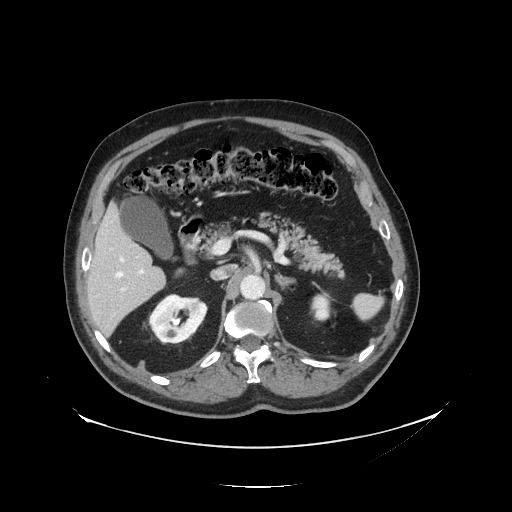
Contrast-enhanced abdominal CT, one axial slice; position 73 of 138 along the scan axis; intravenous contrast given; soft-tissue window (W 400 / L 40 HU); 2.5 mm slice thickness; 512 × 512 image matrix. Male patient, age 77 years. Case-level facts recorded for this patient, not image findings: diagnosis: colorectal cancer liver metastases, imaged before liver resection; multiple liver metastases: no; largest metastasis: 1.5 cm.
Outlined on this slice (expert manual segmentation):
- hepatic veins: box from (x=116, y=258) to (x=124, y=278) px
- liver: (x=87, y=209)–(x=166, y=336)
- planned liver remnant (the part of the liver to remain after resection): (x=87, y=208)–(x=154, y=287)
- portal vein (with intrahepatic branches): (x=121, y=269)–(x=145, y=292)